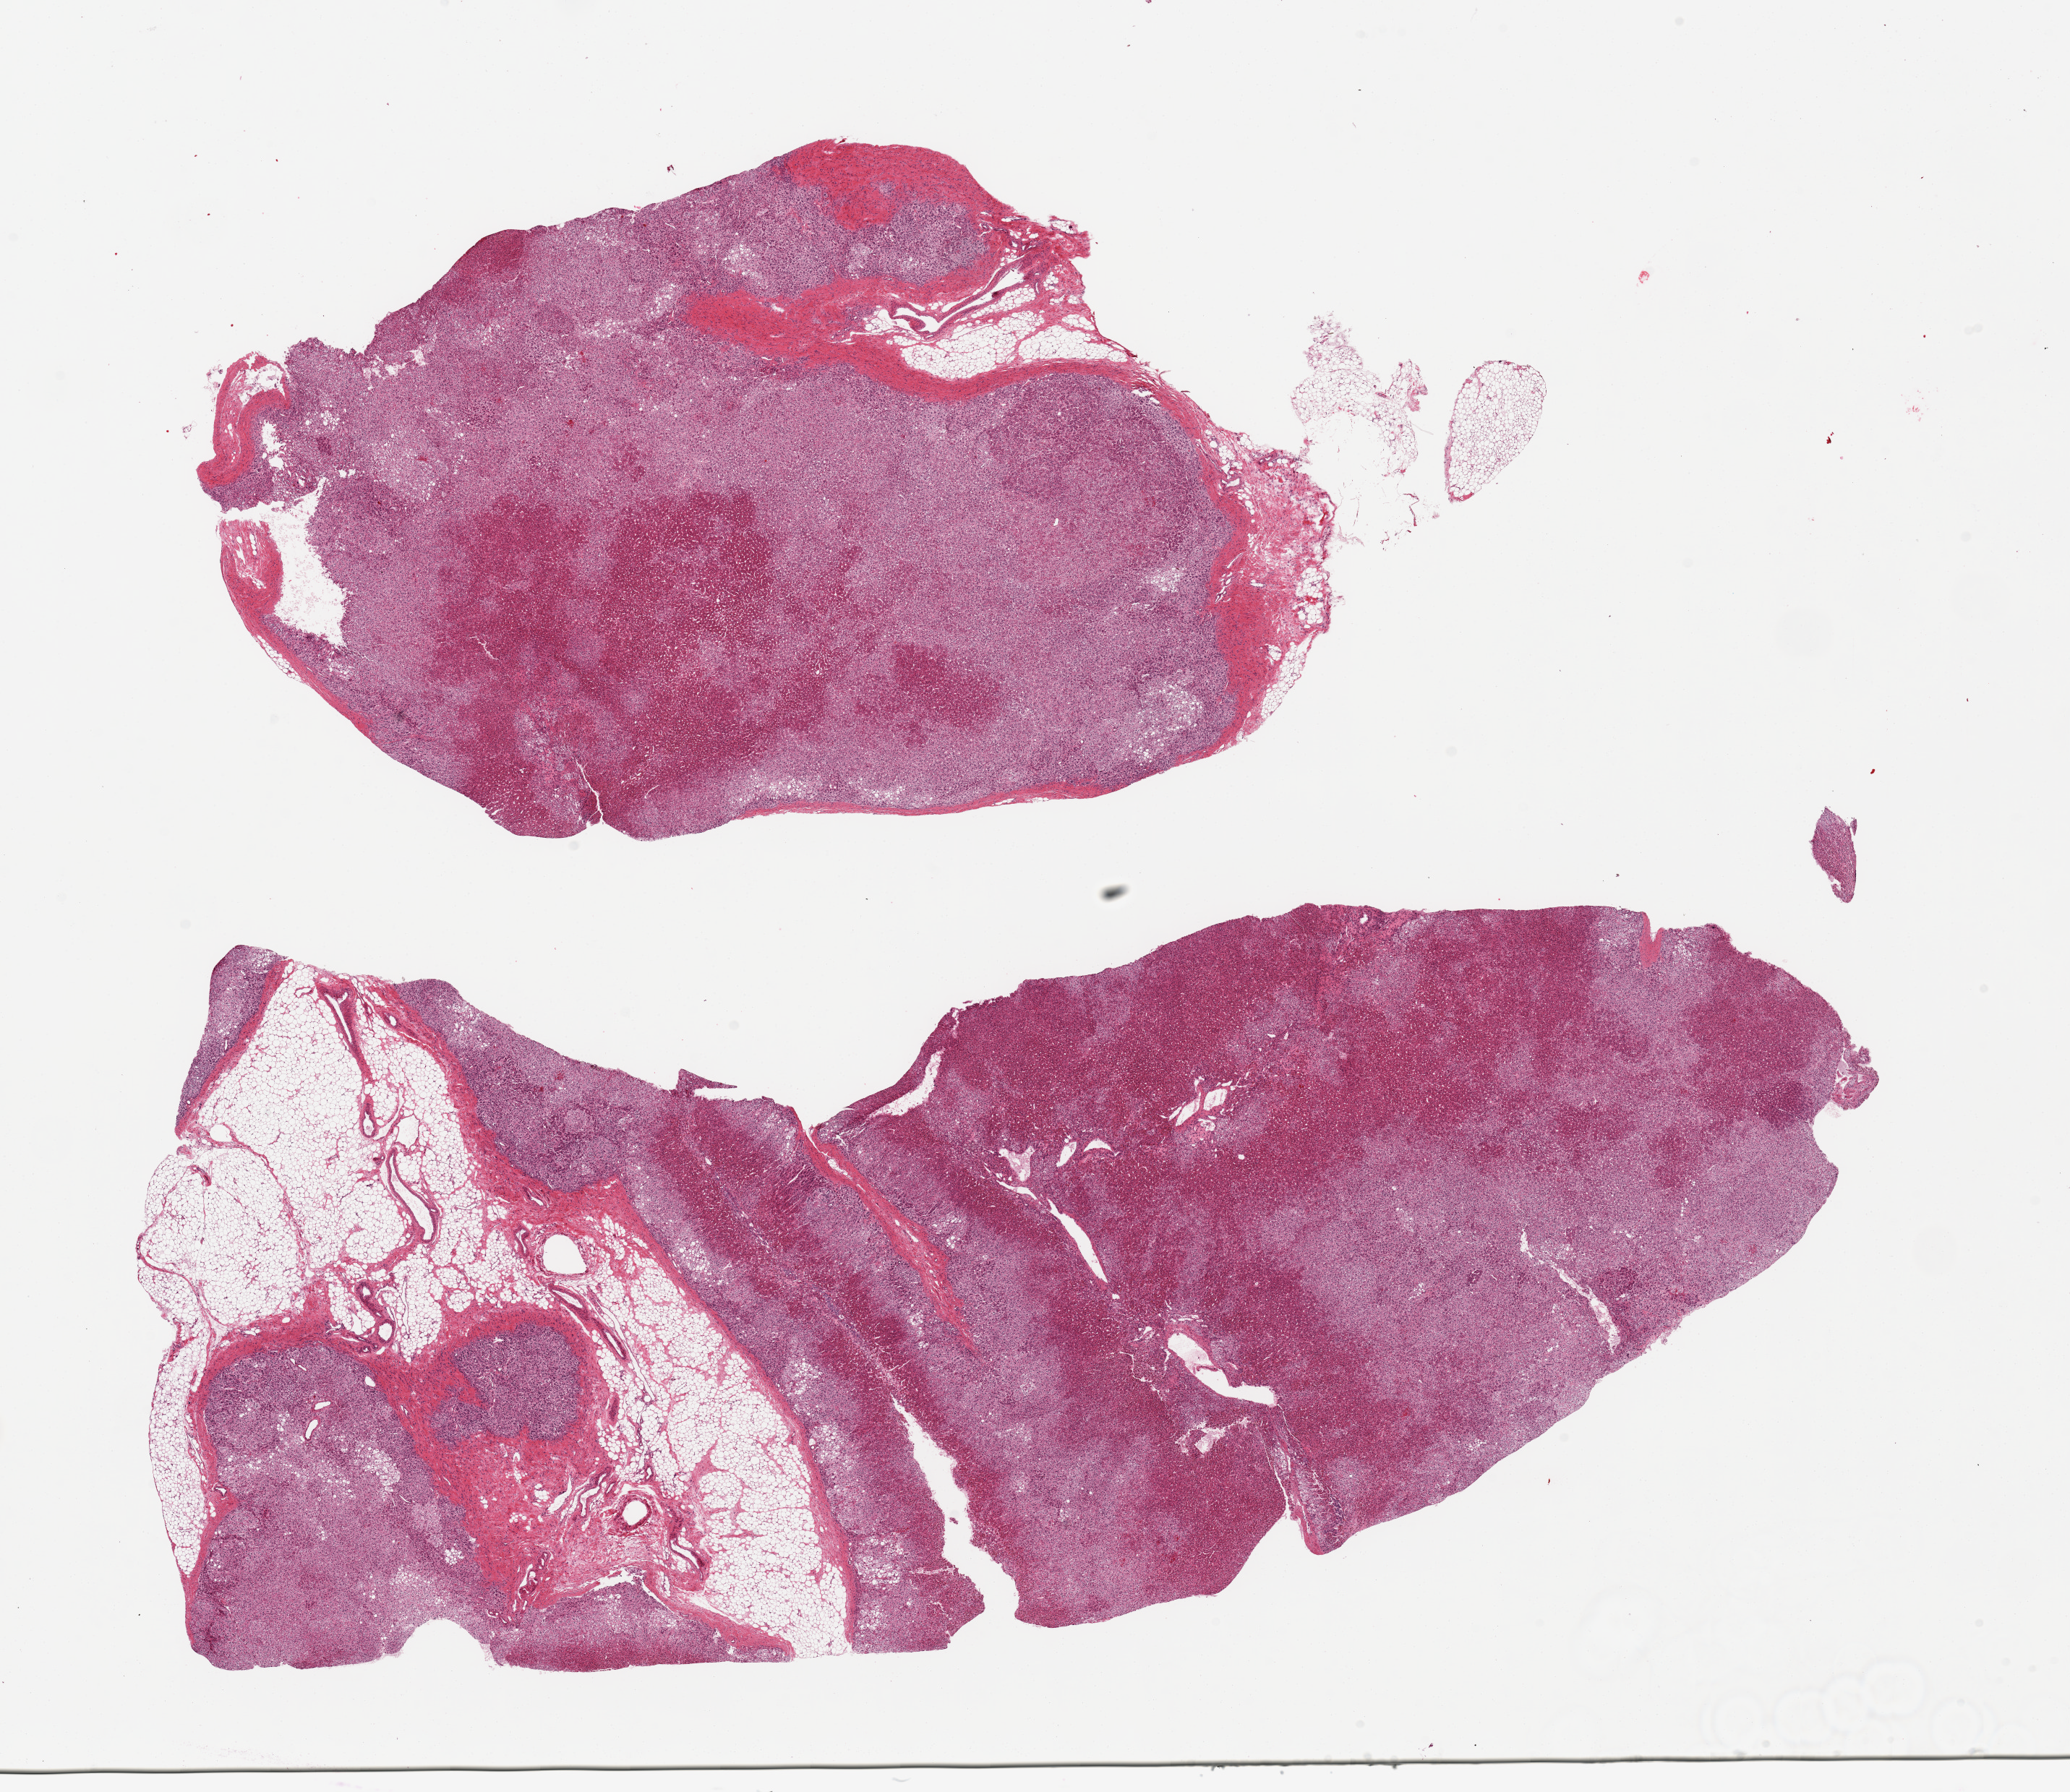
Whole-slide image, H&E stain, whole scanned area (about 22.6 x 19.6 mm, from a 20x scan) shown as a low-resolution overview, PAXgene-fixed paraffin-embedded (PFPE) section, section of adrenal gland (target tissue), donor tissue sample.
Pathologist's review note for this sample: 2 pieces; oversized, ~15% of one piece is fat.